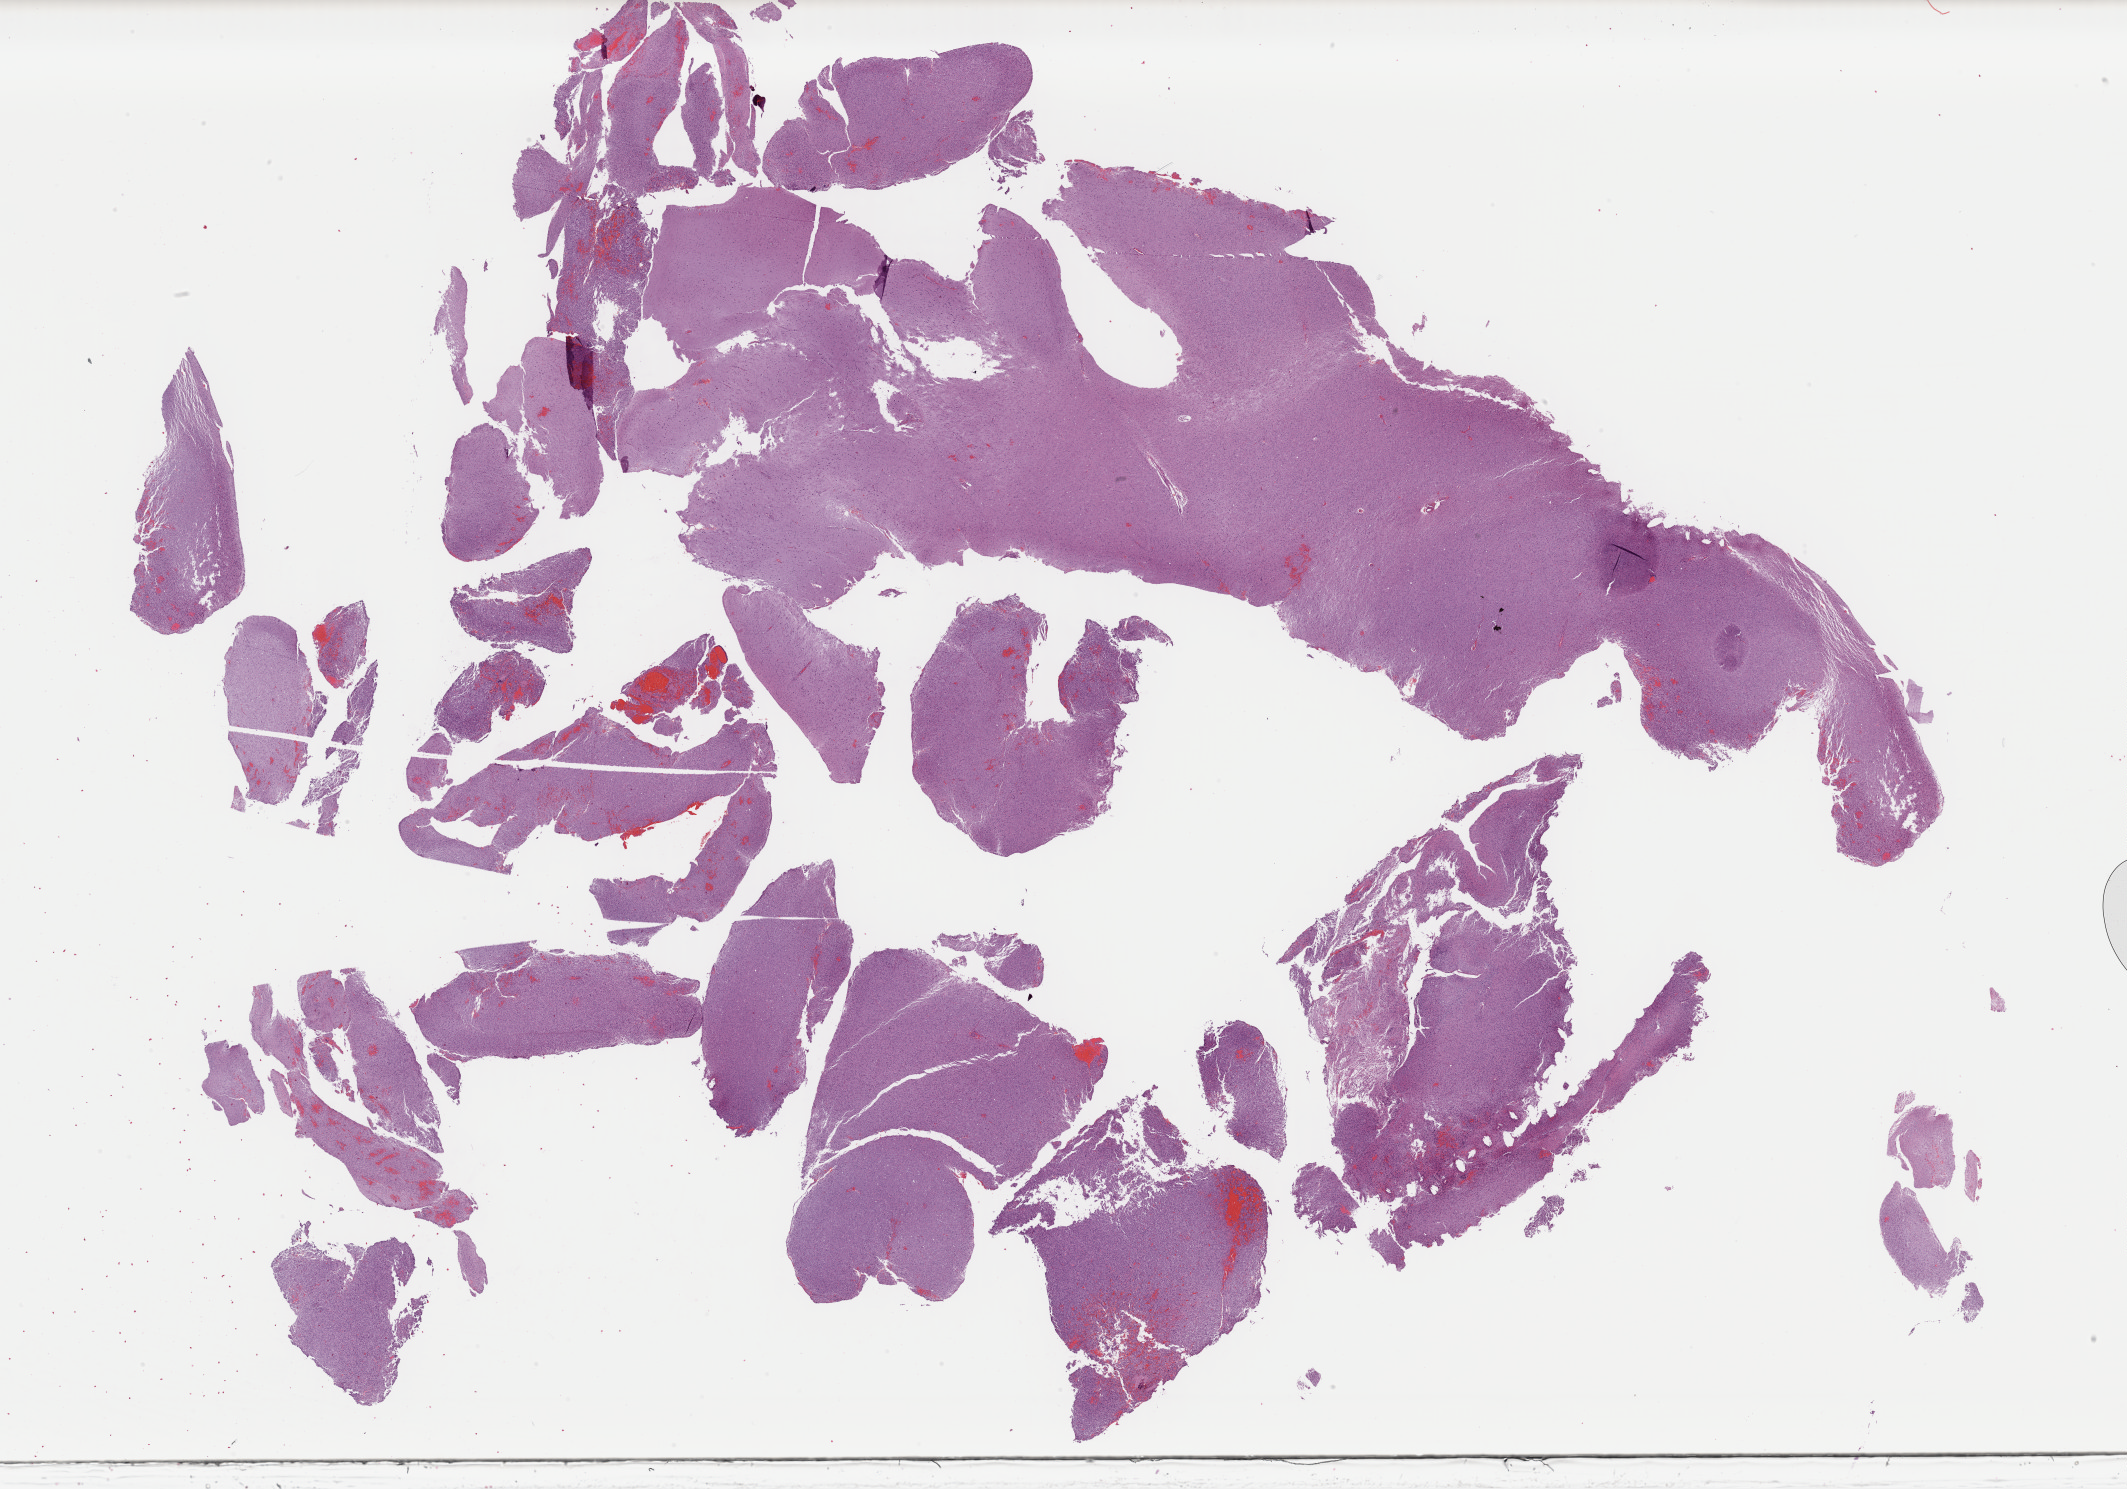
Digitized H&E tissue section (whole slide) — shown as a low-resolution overview of the whole scanned area (about 33.6 x 23.5 mm); formalin-fixed paraffin-embedded (FFPE) diagnostic section; brain, primary tumour sample. Female patient; age at initial diagnosis 55 years. Histologic grade: G3 (poorly differentiated).
Pathologic diagnosis: Astrocytoma, anaplastic (cerebrum).